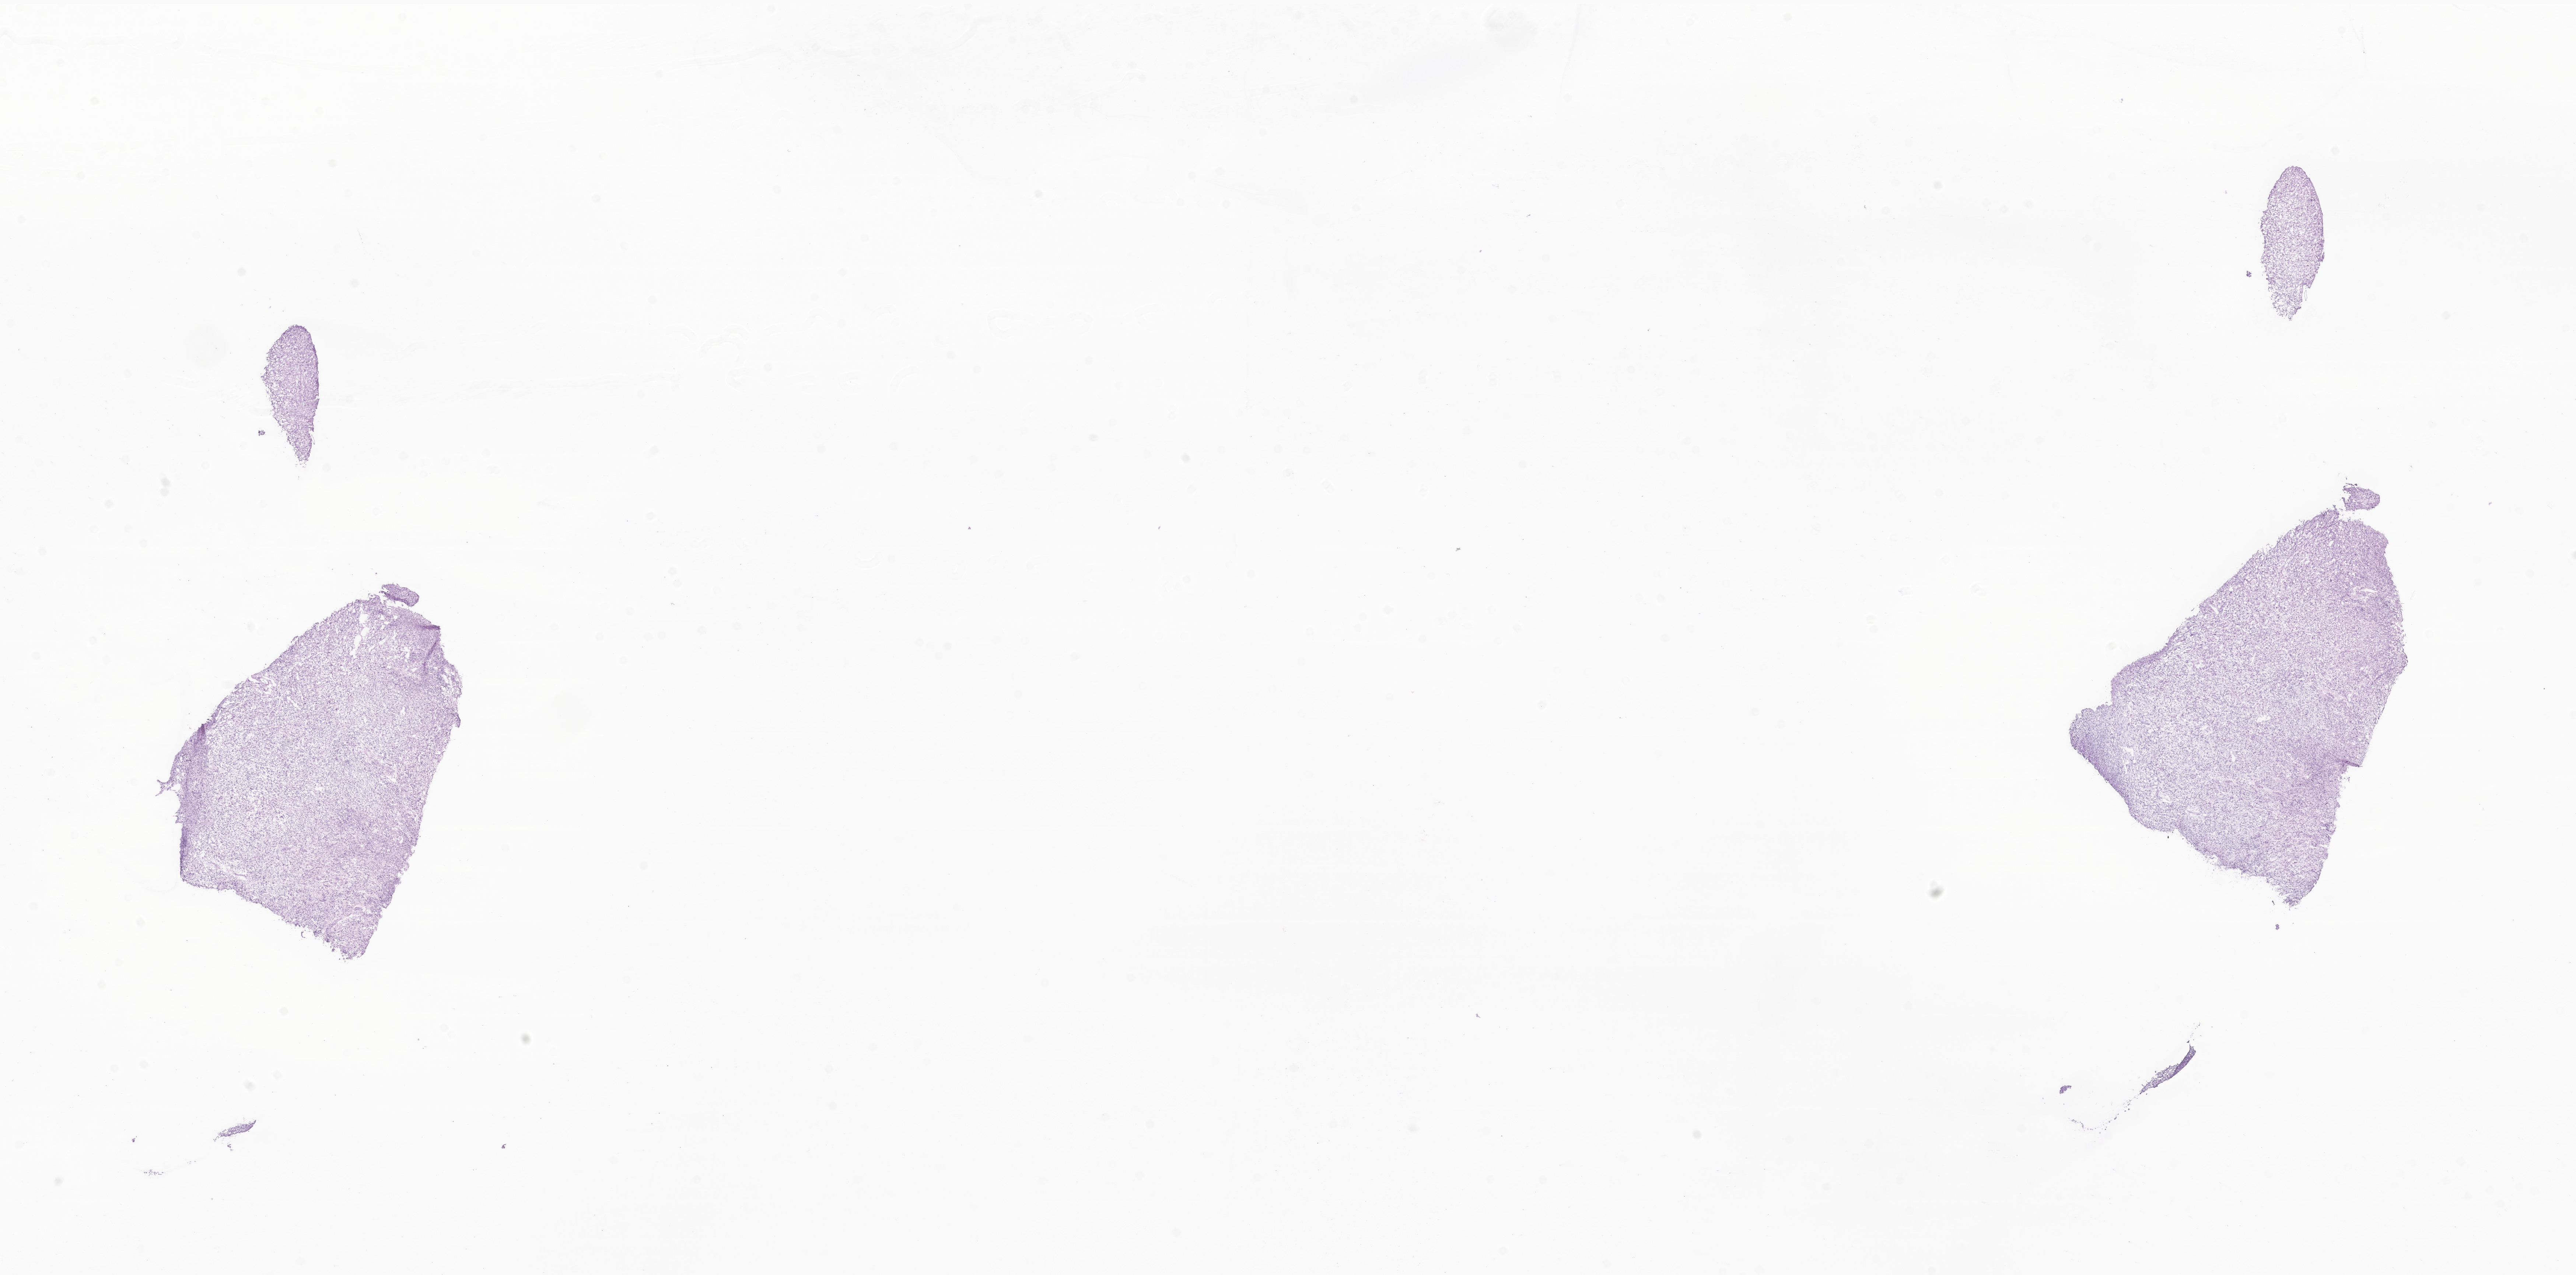
Haematoxylin and eosin whole-slide image of tumor tissue from the scrotum — a low-resolution overview of the entire scanned area, about 29.5 x 14.6 mm. Frozen section (OCT-embedded). Male patient, age 48 months.
Diagnosis: Embryonal rhabdomyosarcoma, NOS.